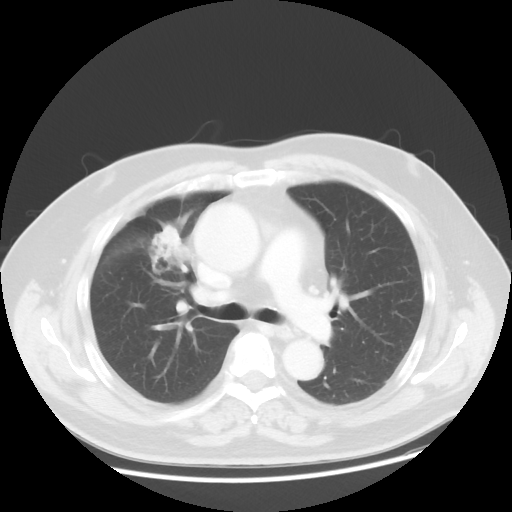
Chest CT, one axial slice. Position 29 of 48 along the scan axis. 120 kVp. Lung window (W 1500 / L -600 HU). 5 mm slice thickness. 512 × 512 image matrix, field of view 392 × 392 mm. Male patient, age 60 years. From the clinical record (not read from this slice): clinical TNM (as recorded): T2 N3 M0.
Outlined on this slice (bounding box drawn by a radiologist):
- lung tumour (recorded histology: adenocarcinoma): bounding box (x1, y1, x2, y2) in pixels: (141, 219, 194, 285)